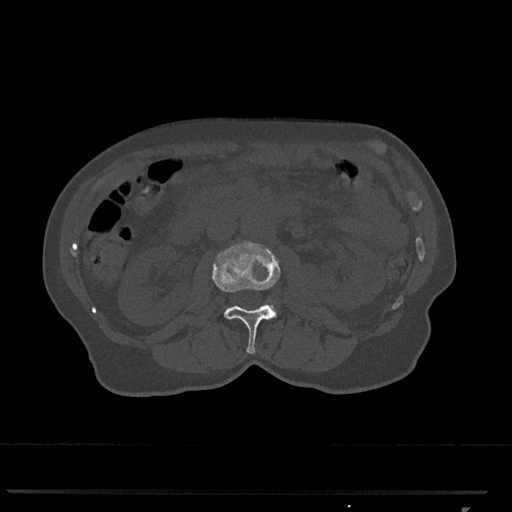
CT including the spine, one axial slice; position 322 of 793 along the scan axis; 120 kVp; bone window (W 1800 / L 400 HU); 0.5 mm slice thickness; 512 × 512 image matrix. Patient: female, 62 years. Case-level facts recorded for this patient, not image findings: primary cancer: renal.
Annotated regions visible in this slice (semi-automatic segmentation, software-assisted and operator-edited):
- L2 vertebra: box from (x=212, y=242) to (x=281, y=354) px